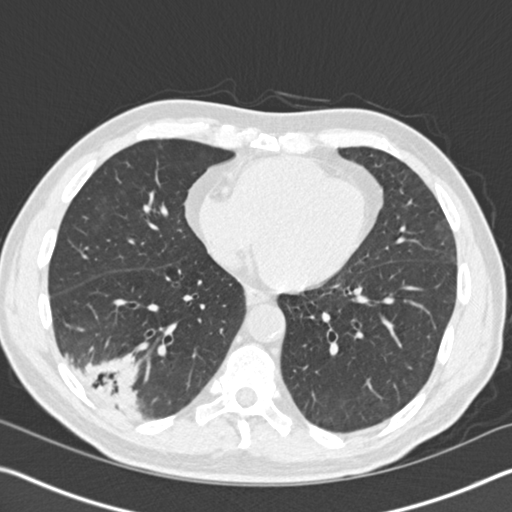
Chest CT (low-dose screening protocol), one axial image; baseline screening round; lung window (W 1500 / L -600 HU); 120 kVp; slice 100 of 161 in the series; 512 × 512 image matrix, field of view 340 × 340 mm. Male participant, aged 61 years at enrolment. Current smoker at enrolment.
Expert reader's lesion annotation, bounding box <41,317,154,422> (left, top, right, bottom; pixels). Screening reader's record for this exam (one nodule recorded; not confirmed to be the boxed lesion): non-calcified nodule or mass ≥4 mm, right lower lobe, 52 × 36 mm, spiculated (stellate) margins, soft tissue attenuation. Official screen result: positive, change unspecified: nodule(s) >= 4 mm or enlarging nodule(s), mass(es), or other non-specific abnormalities suspicious for lung cancer. Participant outcome: lung cancer diagnosed 392 days after this screen (after the second annual screen) — bronchiolo-alveolar adenocarcinoma, NOS, right lower lobe, moderately differentiated (G2), stage IIIB (AJCC 6th edition), 90 mm at pathology.